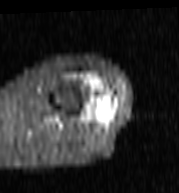
MRI of an extremity soft-tissue mass, one axial slice. Position 26 of 103 along the scan axis. STIR. MR volume resampled by the dataset authors to the PET/CT grid (not the native acquisition matrix). 179 × 193 image matrix, field of view 175 × 188 mm. Female patient. Case-level facts recorded for this patient, not image findings: histological type: undifferentiated – high grade; grade: high; site of the primary tumour: left thigh.
Structures marked on this image (expert contour drawn on MRI and transferred to this co-registered scan by the dataset authors):
- gross tumour volume including surrounding oedema: bounding box <93,98,110,111> (left, top, right, bottom; pixels)